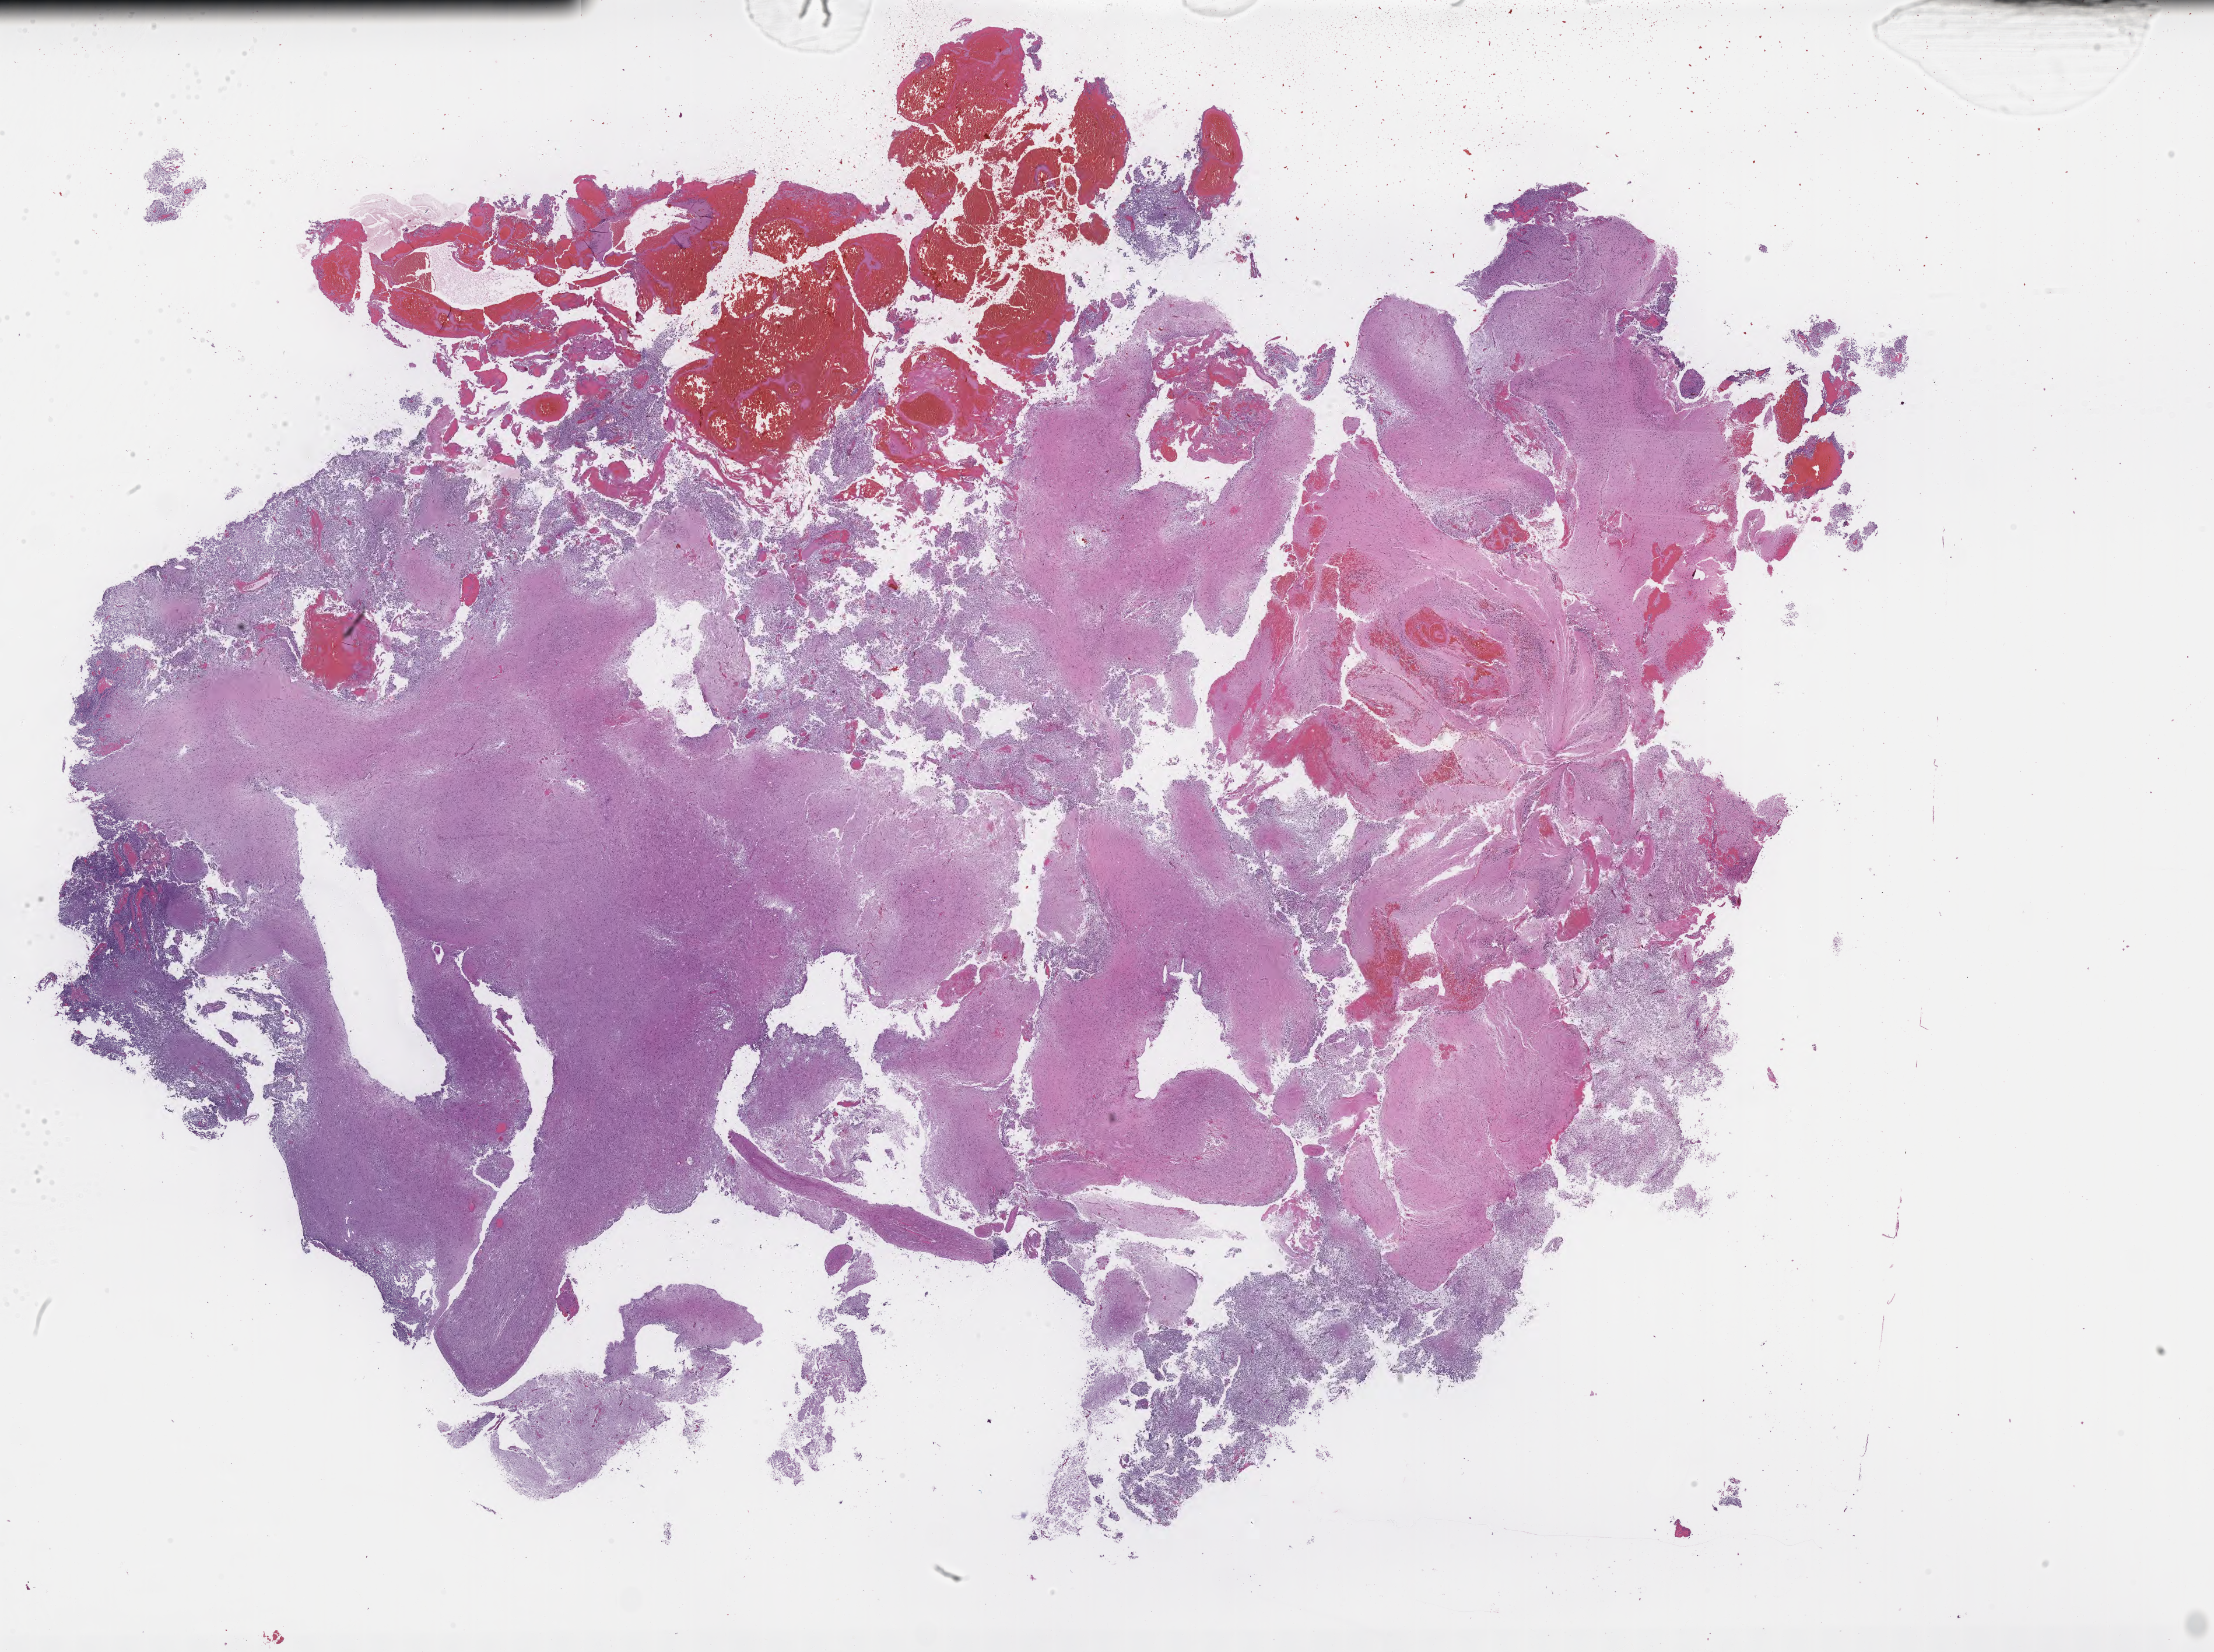
Digitized hematoxylin and eosin (H&E)-stained section of tumor tissue from the brain, a low-resolution overview of the entire scanned area, about 30.7 x 22.9 mm; FFPE section. Male patient, age 57 months (4 years 9 months).
Recorded diagnosis: Neoplasm, malignant.